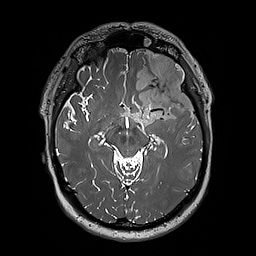
Brain MRI from a brain-tumour surgery series, one axial slice. Slice 123 of 192 in the series (ordered by position). 256 × 256 image matrix, field of view 250 × 250 mm. Case-level facts recorded for this patient, not image findings: histopathology: Oligodendroglioma; WHO grade: 3.
Structures marked on this image (outlined manually by an expert reader):
- tumour: bounding box <124,52,197,125> (left, top, right, bottom; pixels)